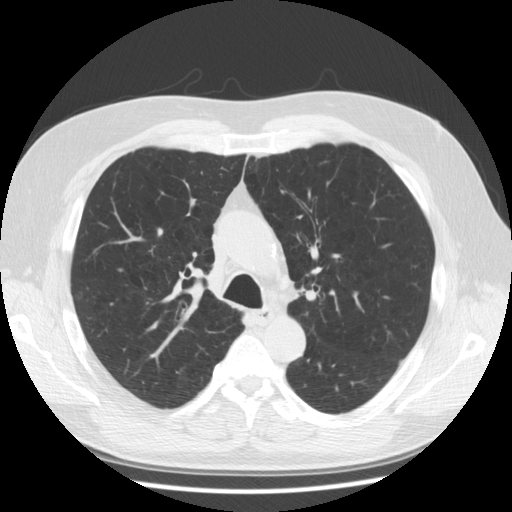
Chest CT (low-dose screening protocol), one axial image. Second screening round (one year after baseline). Lung window (W 1500 / L -600 HU). 2.5 mm slice thickness. Standard (soft-tissue) reconstruction kernel (STANDARD). Slice 58 of 173 in the series. Male, age 63 years at enrolment. Former smoker at enrolment.
Lesion marked by an expert reader, bounding box [x1, y1, x2, y2] px = [144, 220, 176, 245]. No non-calcified nodule or mass ≥4 mm was recorded by the screening reader at this exam. Official screen result: negative screen, no significant abnormalities. Later outcome: lung cancer diagnosed 717 days after this screen (after the third annual screen) — adenocarcinoma, NOS, right upper lobe, stage IIA (AJCC 6th edition), 8 mm at pathology.